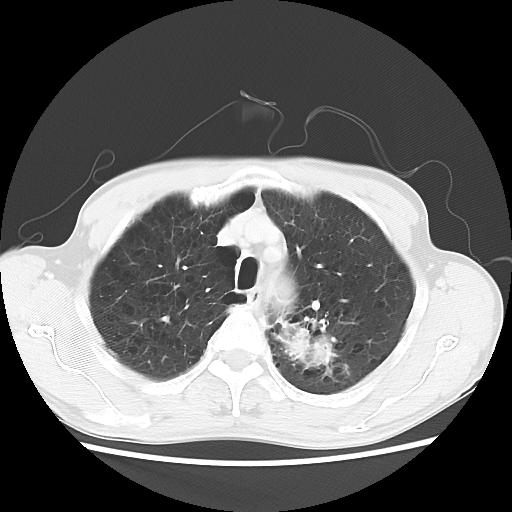
Chest CT, one axial slice; position 50 of 64 along the scan axis; 120 kVp; lung window (W 1500 / L -600 HU); 512 × 512 image matrix, field of view 346 × 346 mm. Patient: male, 63 years. From the clinical record (not read from this slice): clinical TNM (as recorded): T2 N0 M0.
Structures marked on this image (bounding box drawn by a radiologist):
- lung tumour (recorded histology: adenocarcinoma): bounding box (x1, y1, x2, y2) in pixels: (281, 321, 336, 377)